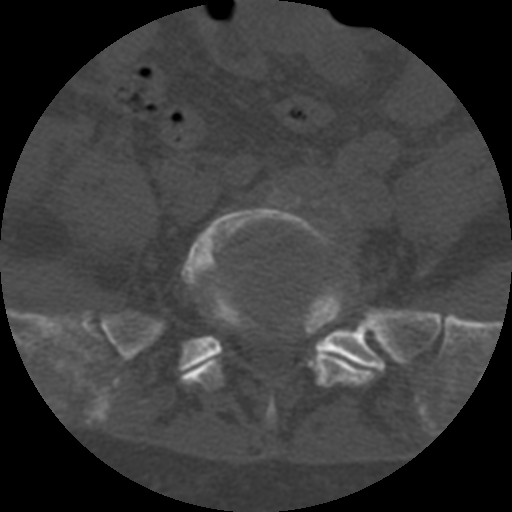
CT including the spine, one axial slice; slice 176 of 708 in the series (ordered by position); one of 3 acquisitions stored at this slice position; bone window (W 1800 / L 400 HU); 1.25 mm slice thickness; 512 × 512 image matrix, field of view 160 × 160 mm. Patient age 55 years. Case-level facts recorded for this patient, not image findings: primary cancer: colon; vertebrae with lytic lesions (as recorded): T12, L1, L5.
Outlined on this slice (semi-automatically segmented with operator editing):
- L5 vertebra: bounding box <181,195,375,425> (left, top, right, bottom; pixels)